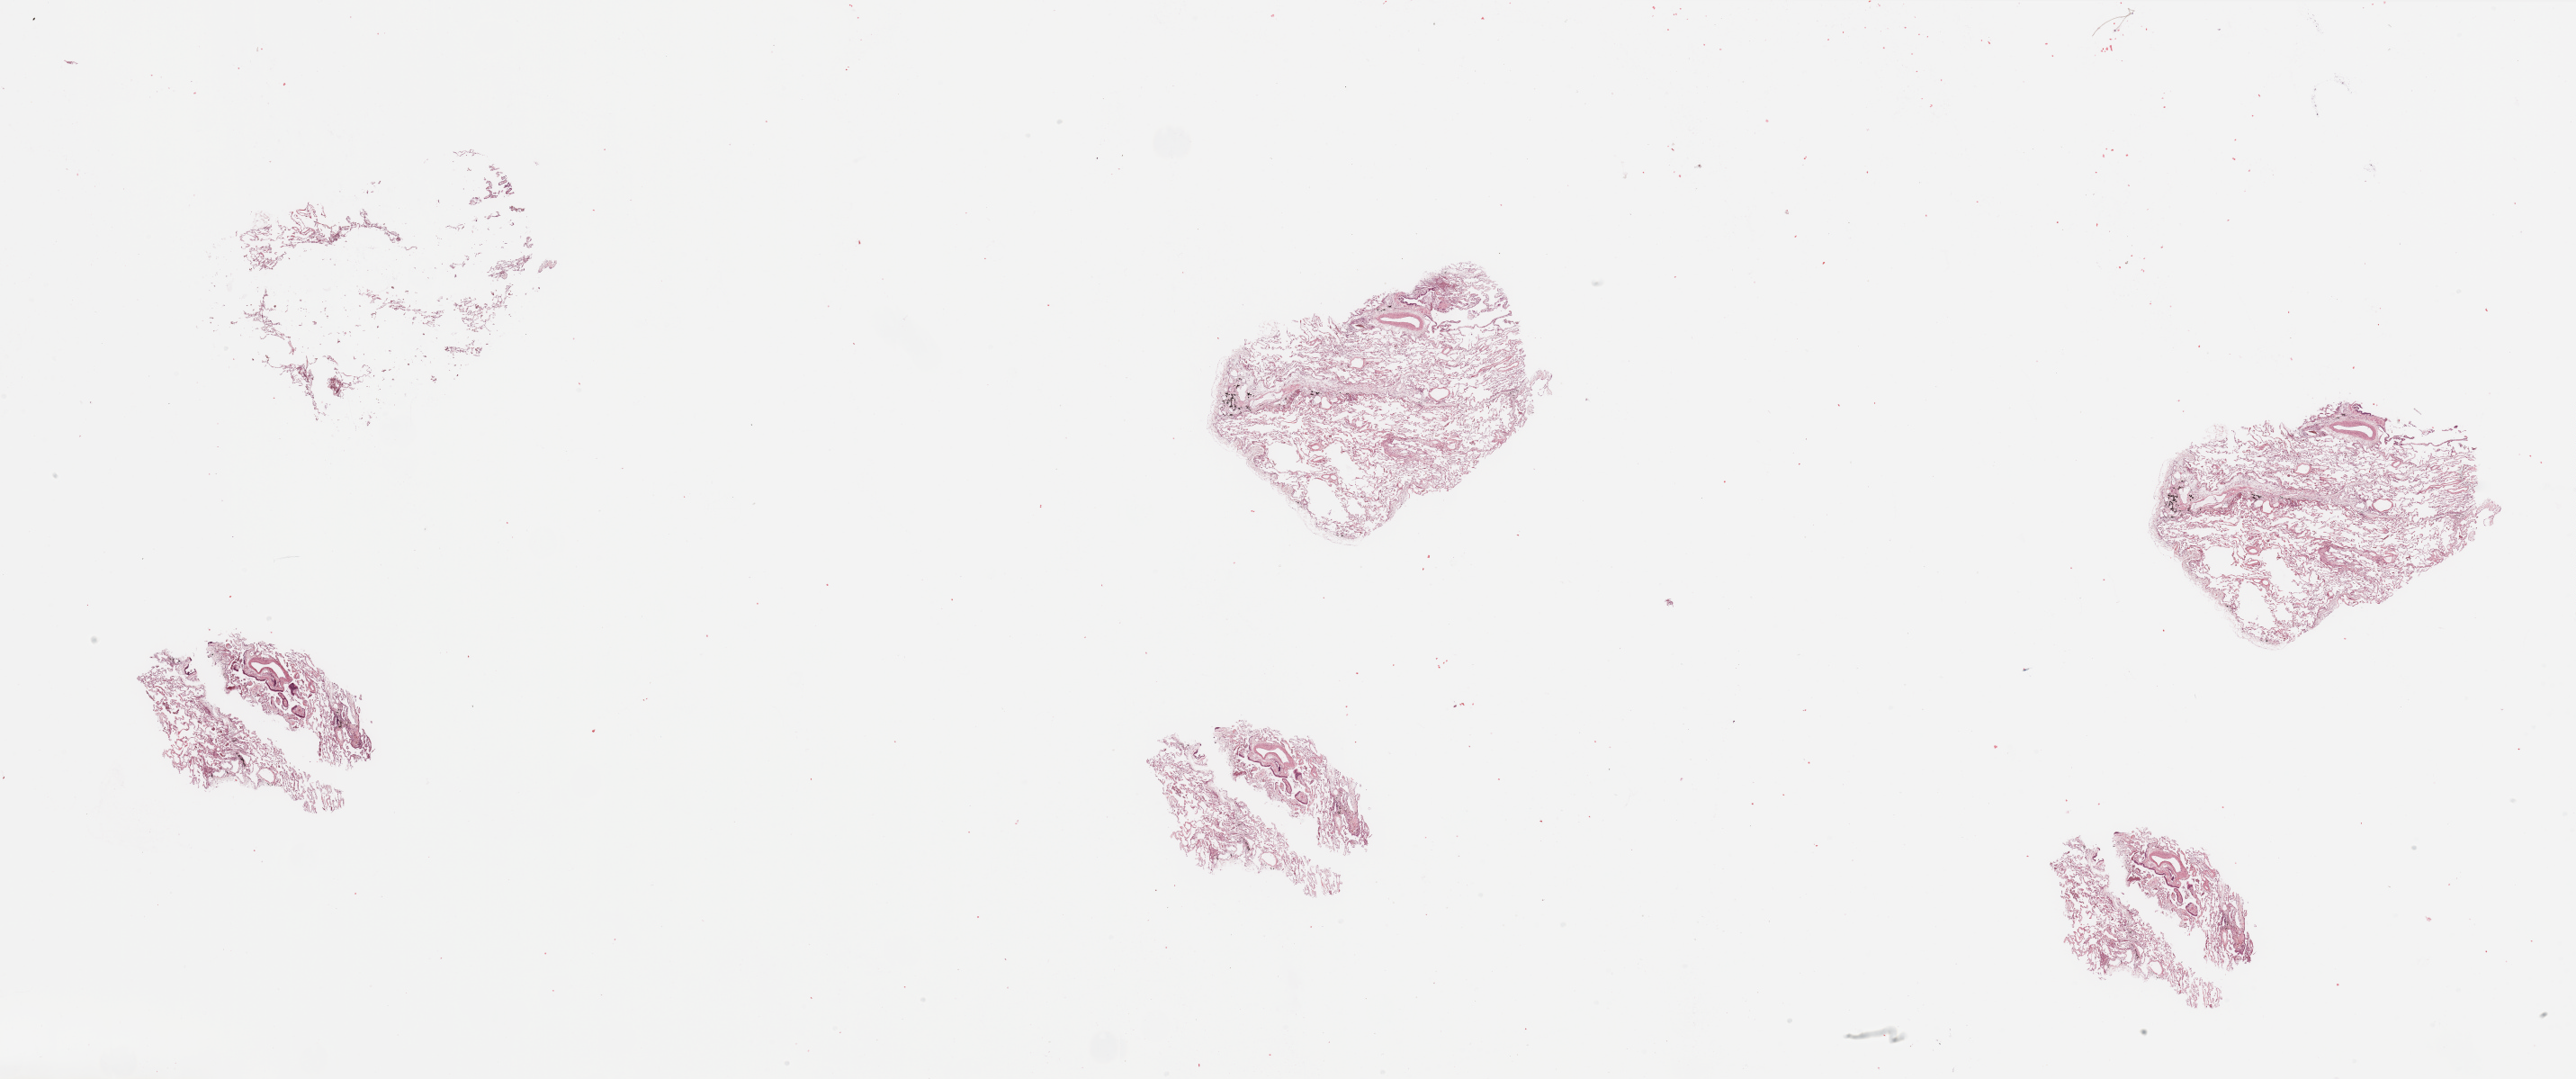
Hematoxylin and eosin (H&E) stained whole-slide image — low-resolution overview of the scanned area, about 45.3 x 19.0 mm (acquisition: 20x scan), normal (non-tumour) tissue sample, sampled site: lung. Male, 69 y/o.
This section: normal (non-tumour) tissue from the same patient. Patient diagnosis: Adenocarcinoma, NOS.